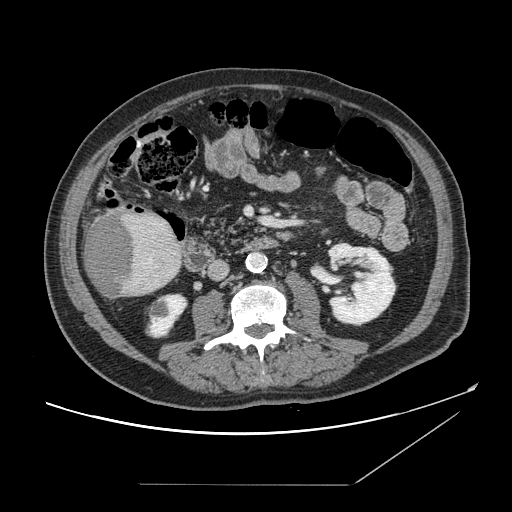
Contrast-enhanced abdominal CT, one axial slice; position 44 of 166 along the scan axis; 120 kVp; intravenous contrast given; soft-tissue window (W 400 / L 40 HU); 512 × 512 image matrix, field of view 416 × 416 mm. Male patient, age 80 years. From the clinical record (not read from this slice): diagnosis: colorectal cancer liver metastases, imaged before liver resection; multiple liver metastases: no; largest metastasis: 2.2 cm; disease in both lobes: no.
Annotated regions visible in this slice (outlined manually by an expert reader):
- liver: bounding box <84,208,183,299> (left, top, right, bottom; pixels)
- liver metastasis: <84,215,135,297>